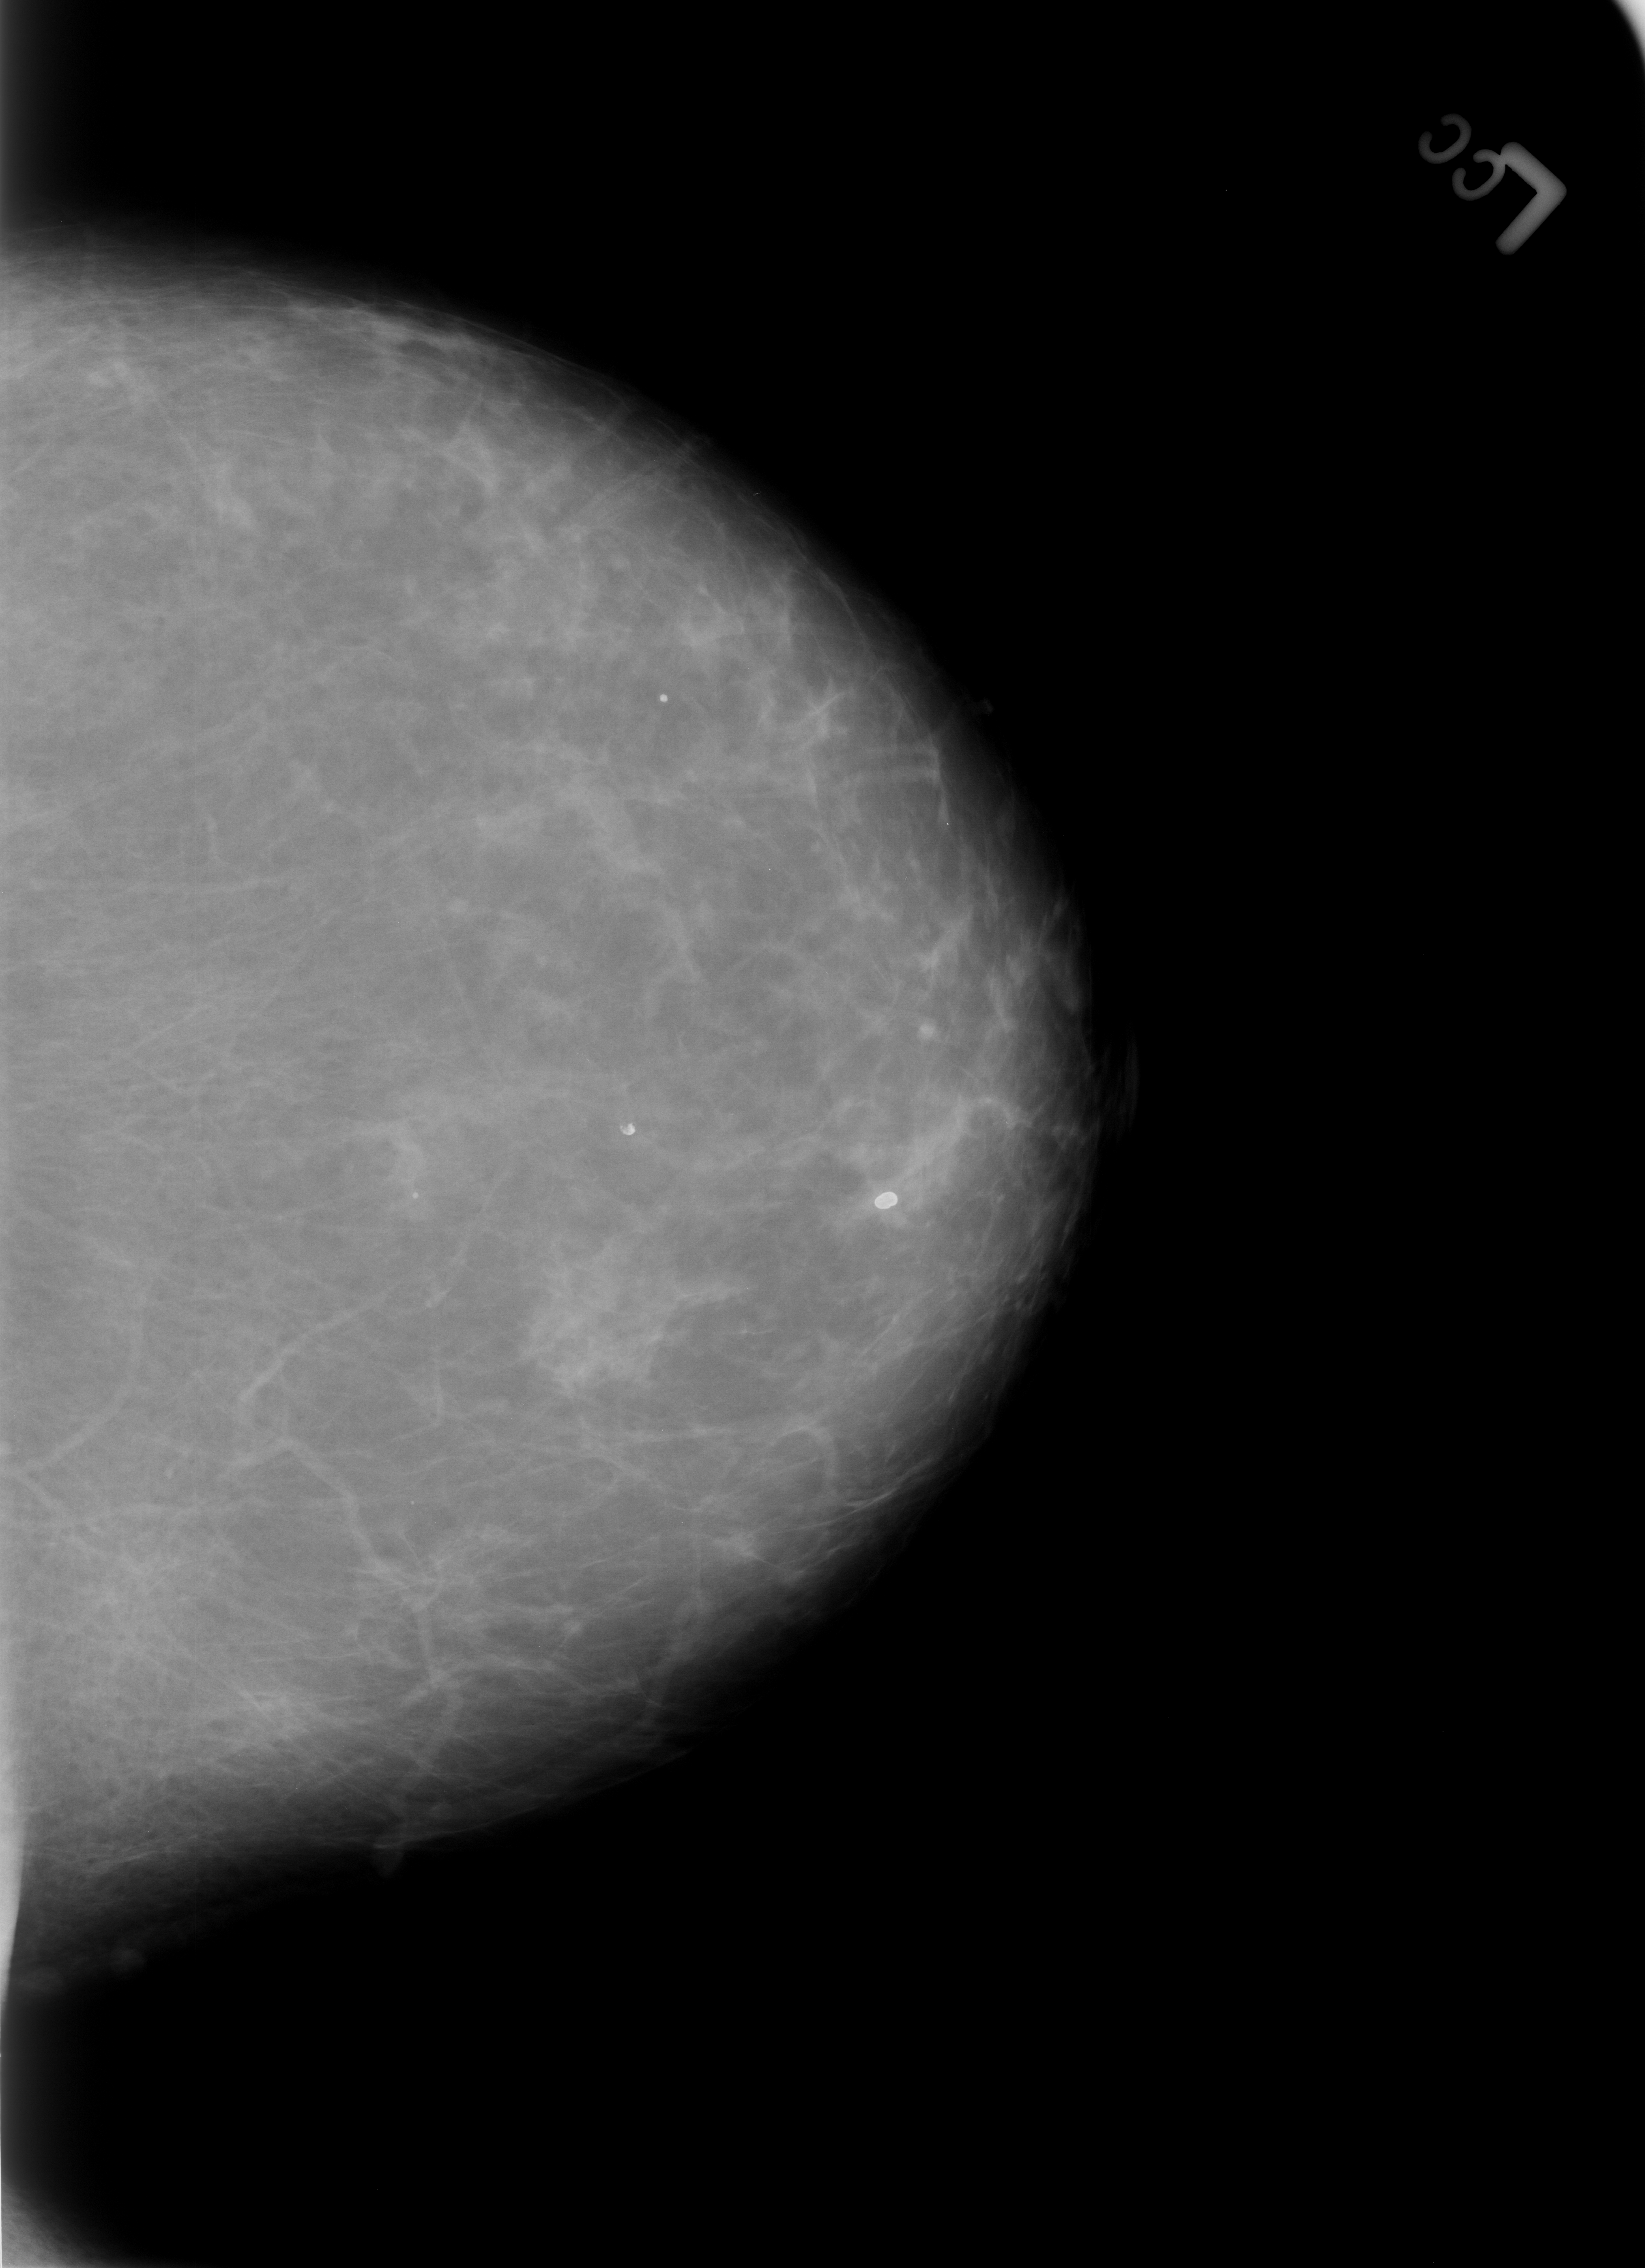
Mammogram (digitized film). Left breast. Craniocaudal (CC) view. Breast composition: scattered fibroglandular densities (BI-RADS density category 2 of 4). 1645 × 2268 image matrix.
Expert-marked regions of interest on this film, with their recorded descriptors:
- Finding 1 of 3: calcifications, morphology lucent center; BI-RADS assessment category 2; subtlety rating 5 on a 1 (subtle) to 5 (obvious) scale; benign; no additional work-up was recommended (outcome (as recorded, no biopsy): benign without callback): bounding box (x1, y1, x2, y2) in pixels: (600, 1103, 669, 1162)
- Finding 2 of 3: calcifications, morphology lucent center; BI-RADS assessment category 2; subtlety rating 5 on a 1 (subtle) to 5 (obvious) scale; outcome (as recorded, no biopsy): benign without callback (not worked up further): (622, 665, 702, 734)
- Finding 3 of 3: calcifications, morphology lucent center; BI-RADS assessment category 2; benign; no additional work-up was recommended (outcome (as recorded, no biopsy): benign without callback): (846, 1174, 916, 1240)